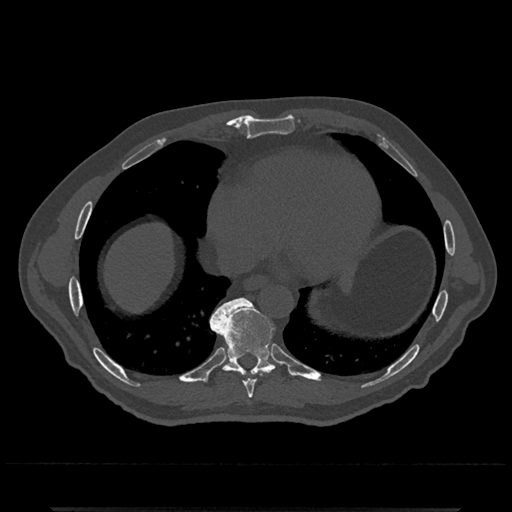
CT including the spine, one axial slice. Slice 635 of 797 in the series (ordered by position). Reconstruction kernel Br40s/3. Bone window (W 1800 / L 400 HU). 0.5 mm slice thickness. 512 × 512 image matrix, field of view 393 × 393 mm. Patient: male, 67 years. From the clinical record (not read from this slice): primary cancer: prostate.
Outlined on this slice (semi-automatic segmentation, software-assisted and operator-edited):
- T8 vertebra: box from (x=244, y=380) to (x=256, y=398) px
- T9 vertebra: (x=210, y=298)–(x=278, y=376)